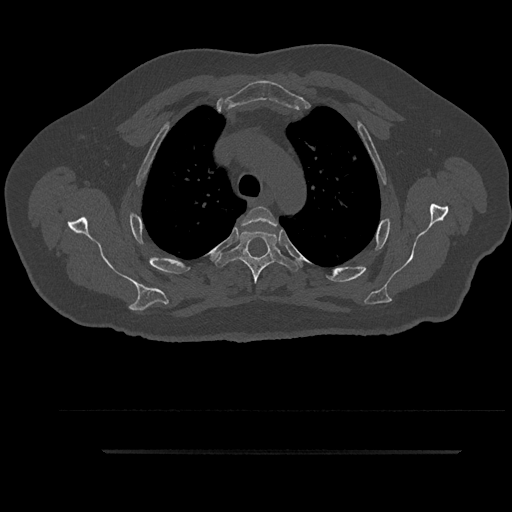
CT including the spine, one axial slice. Slice 683 of 797 in the series (ordered by position). 120 kVp. Bone window (W 1800 / L 400 HU). 0.5 mm slice thickness. 512 × 512 image matrix, field of view 432 × 432 mm. Male patient, age 63 years. From the clinical record (not read from this slice): primary cancer: renal.
Structures marked on this image (semi-automatic segmentation, software-assisted and operator-edited):
- T3 vertebra: bounding box <241,206,278,226> (left, top, right, bottom; pixels)
- T4 vertebra: <215,231,301,284>